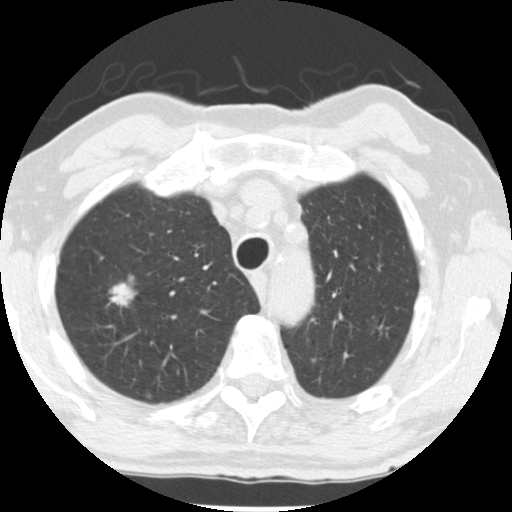
Low-dose screening chest CT, one axial slice; slice 202 of 252 in the series (ordered by position); lung window (W 1500 / L -600 HU); 2.5 mm slice thickness; 512 × 512 image matrix.
Structures marked on this image (outlined manually by an expert reader):
- lesion 1 (tumor, upper lobe of right lung): bounding box [x1, y1, x2, y2] px = [109, 282, 137, 307]